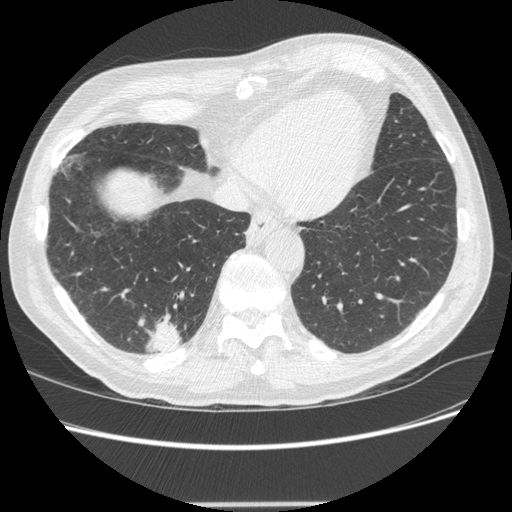
Low-dose screening chest CT, one axial slice. Position 63 of 245 along the scan axis. Reconstruction kernel STANDARD. Lung window (W 1500 / L -600 HU). 1.25 mm slice thickness. 512 × 512 image matrix.
Annotated regions visible in this slice (manually delineated by an expert):
- lesion 1 (tumor, lower lobe of right lung): bounding box [x1, y1, x2, y2] px = [147, 320, 182, 353]